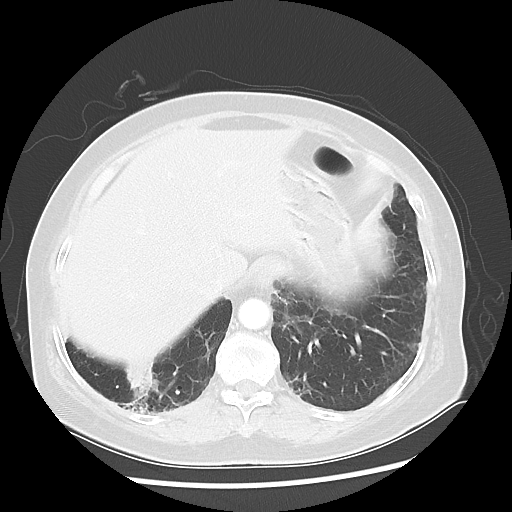
Chest CT, one axial slice. Slice 12 of 56 in the series (ordered by position). Reconstruction kernel LUNG. 120 kVp. Lung window (W 1500 / L -600 HU). 512 × 512 image matrix, field of view 360 × 360 mm. Female patient, age 64 years. Case-level facts recorded for this patient, not image findings: clinical TNM (as recorded): Tis N0 M0.
Annotated regions visible in this slice (bounding box drawn by a radiologist):
- lung tumour (recorded histology: adenocarcinoma): bounding box (x1, y1, x2, y2) in pixels: (116, 350, 185, 421)